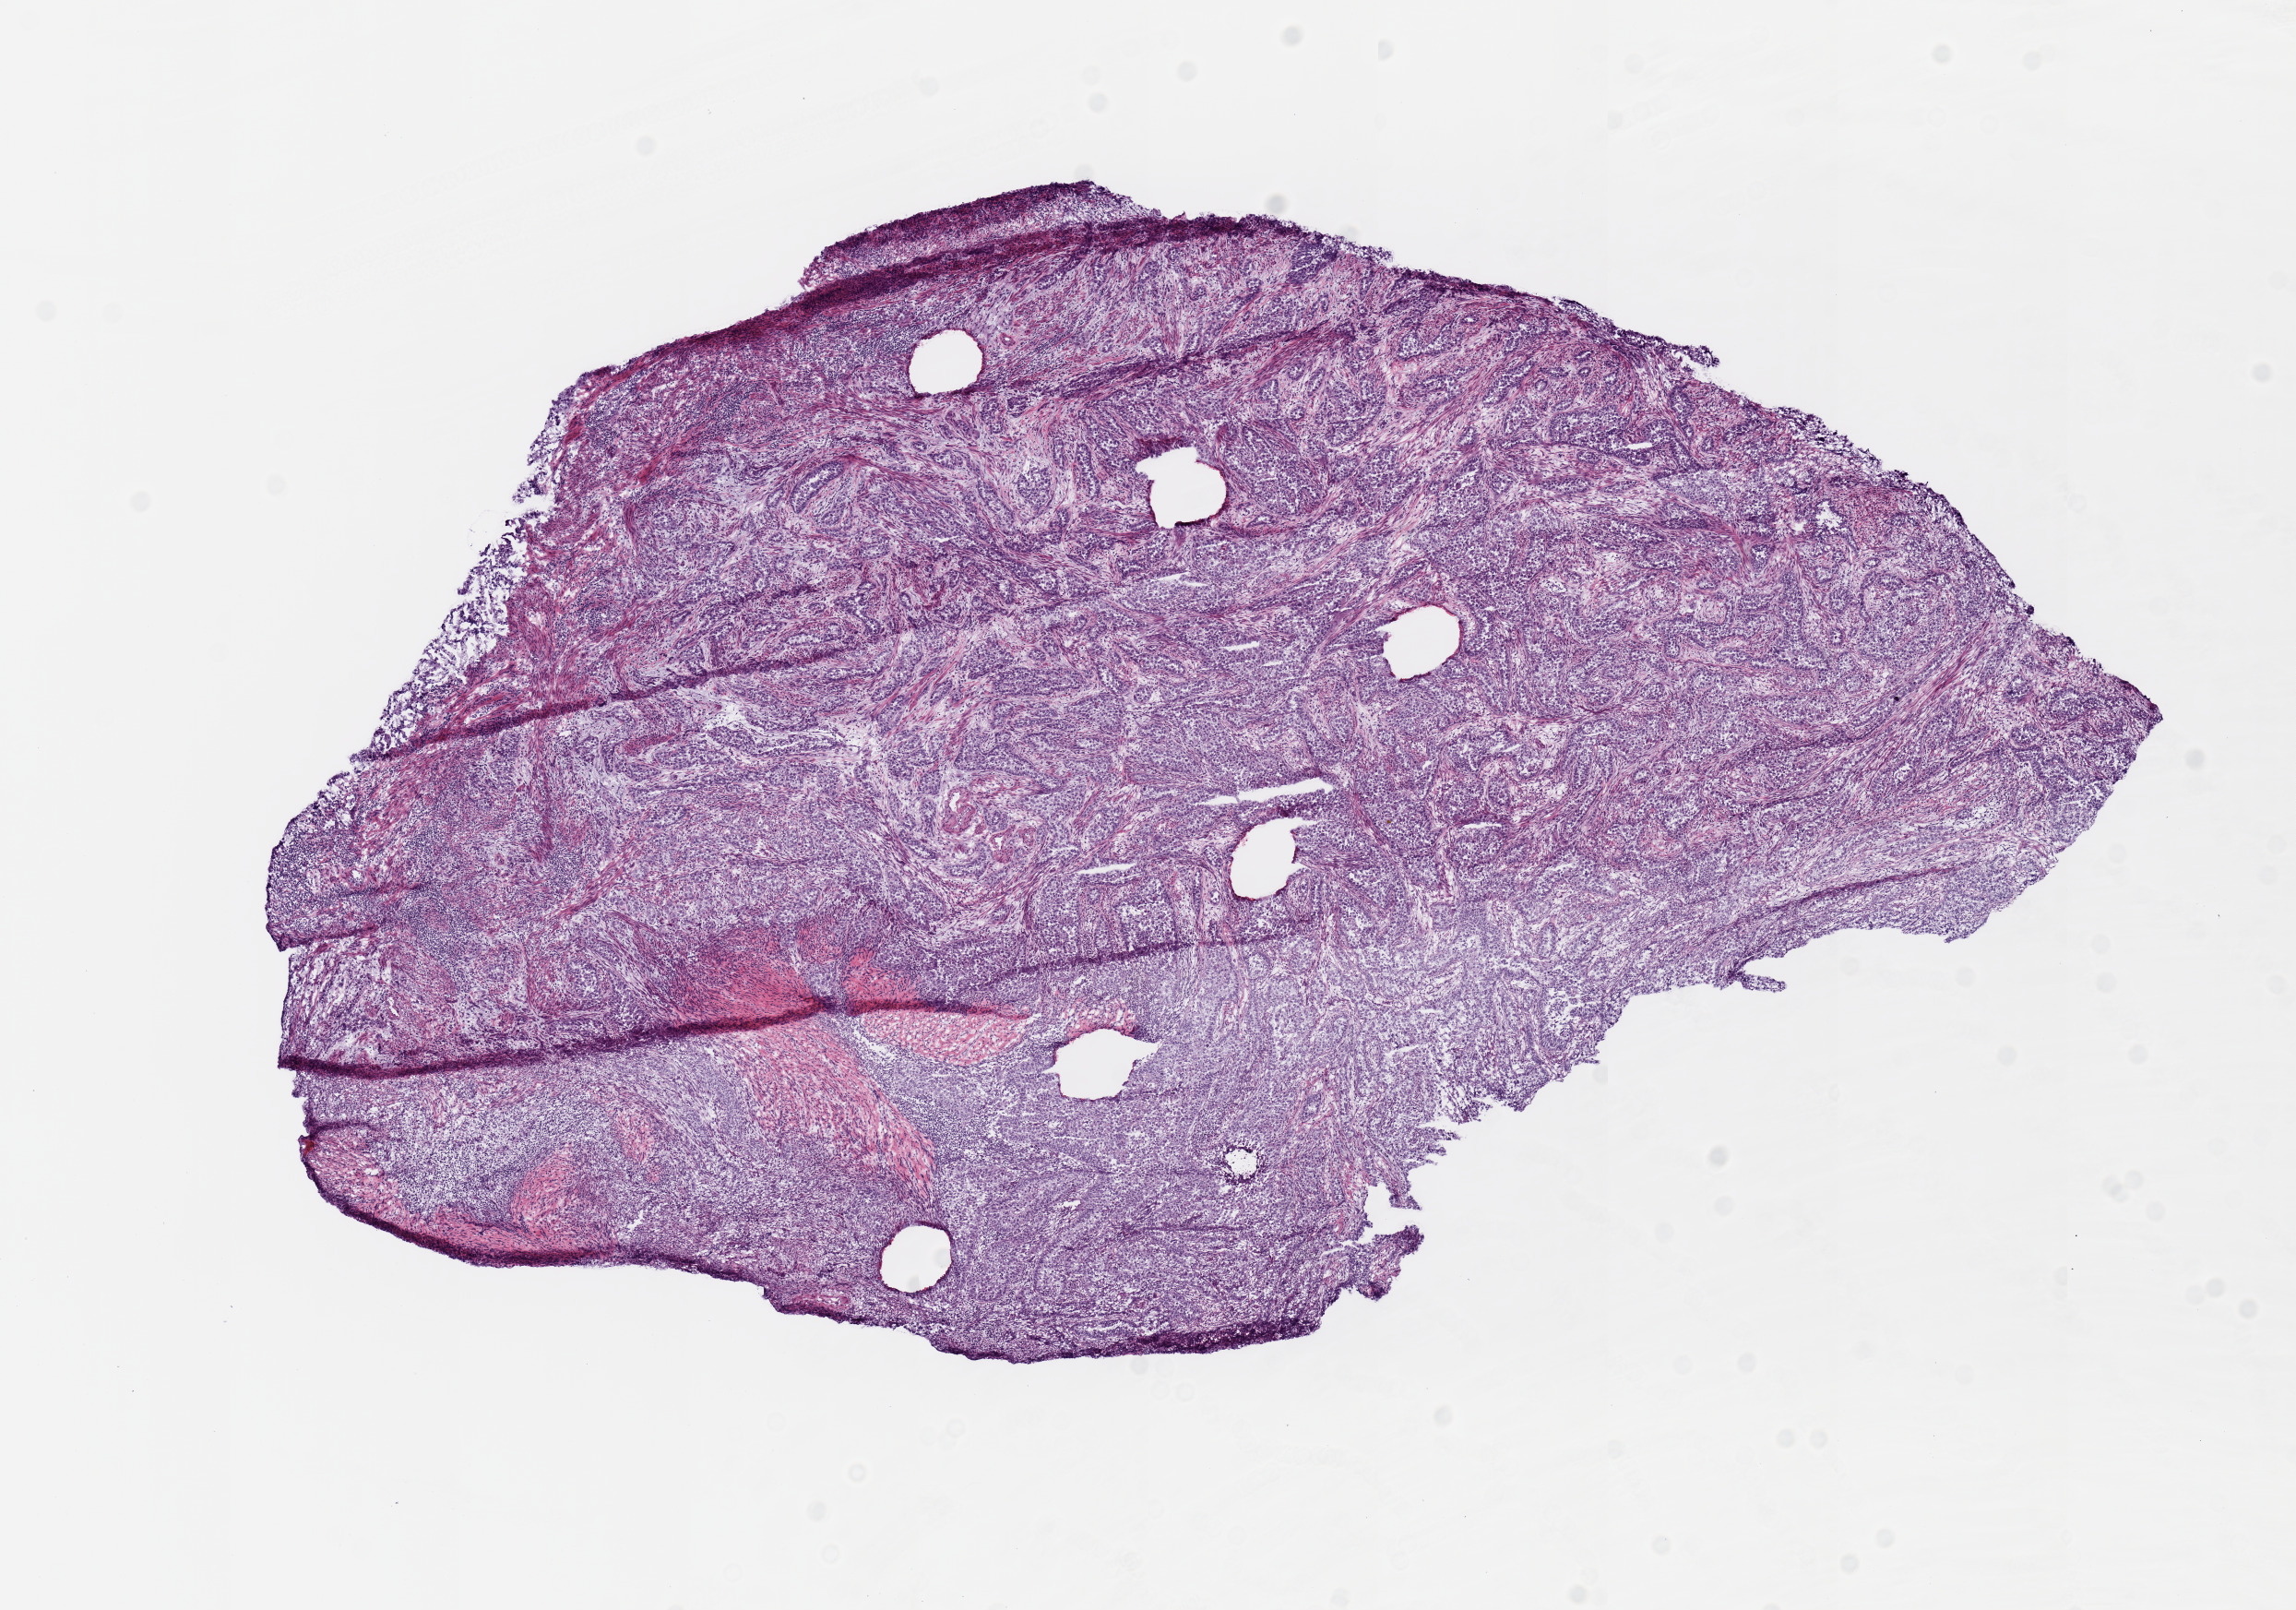
Digitized Hematoxylin and eosin (H&E) stained tissue section (whole slide), whole scanned area (about 9.8 x 6.9 mm, from a 20x scan) shown as a low-resolution overview, frozen section, primary tumour sample from the uterus. Patient: female, age at initial diagnosis 77 years. Histologic grade: G3 (poorly differentiated). Pathologist review of this section (percent, as recorded): tumour cells 90%, tumour nuclei 75%, normal cells 0%, stromal cells 10%, necrosis 0%. Inflammatory infiltration, as recorded: lymphocyte infiltration 0%, monocyte infiltration 0%, neutrophil infiltration 0%.
FIGO stage: IB. Histologic diagnosis: Endometrioid adenocarcinoma, NOS (endometrium).